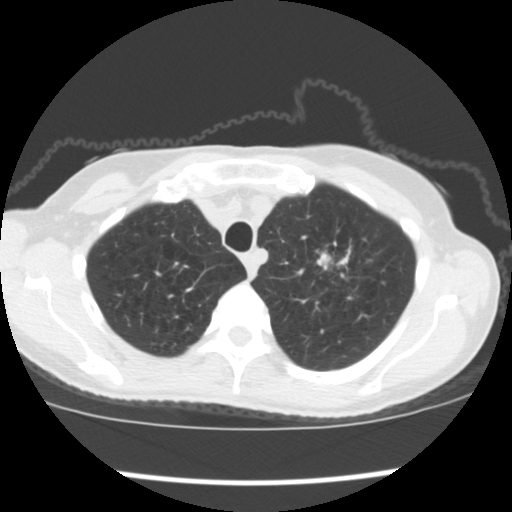
Low-dose screening chest CT, one axial slice. Slice 151 of 176 in the series (ordered by position). Reconstruction kernel STANDARD. Lung window (W 1500 / L -600 HU). 2.5 mm slice thickness. 512 × 512 image matrix, field of view 318 × 318 mm.
Outlined on this slice (expert manual segmentation):
- lesion 1 (tumor, upper lobe of left lung): bounding box [x1, y1, x2, y2] px = [317, 251, 351, 272]